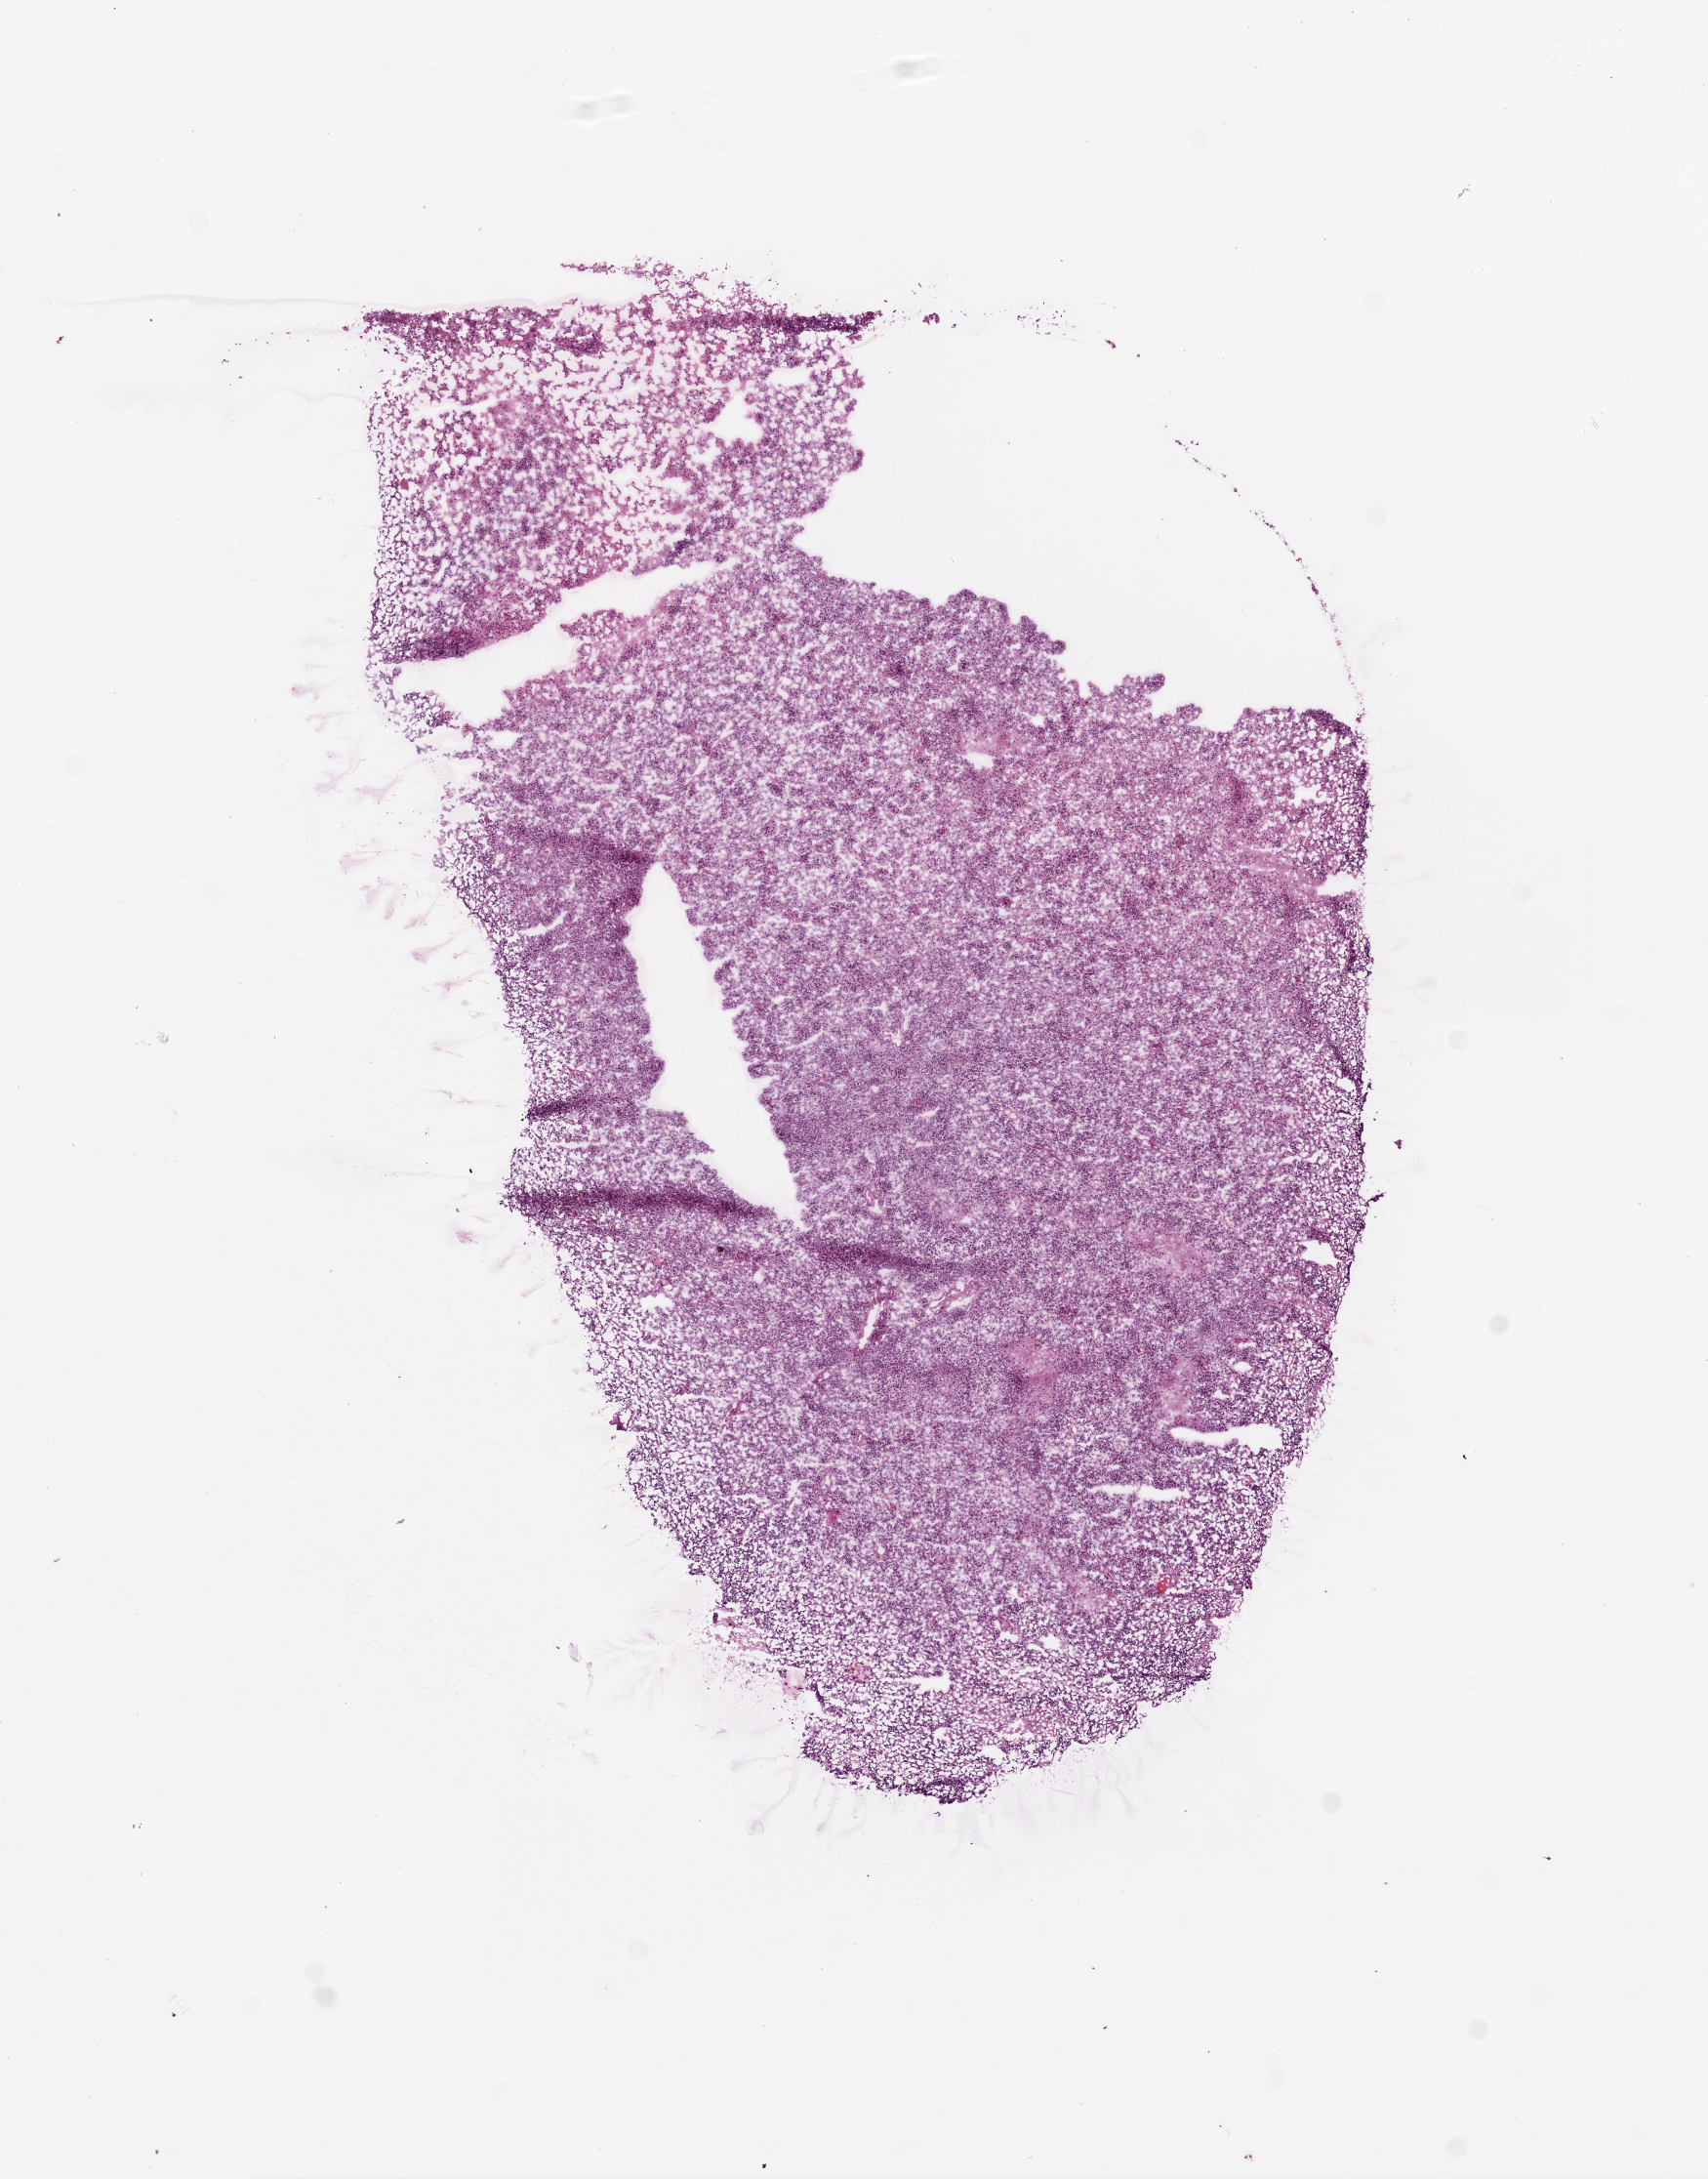
Digitized H&E-stained tissue section (whole slide), whole scanned area (about 7.0 x 9.0 mm, from a 20x scan) shown as a low-resolution overview; frozen section; brain, primary tumour sample. Patient: male, age at initial diagnosis 63 years. Composition of this section per pathologist review: tumour cells 97%, tumour nuclei 85%, normal cells 0%, stromal cells 0%, necrosis 3%.
Histologic diagnosis: Glioblastoma.